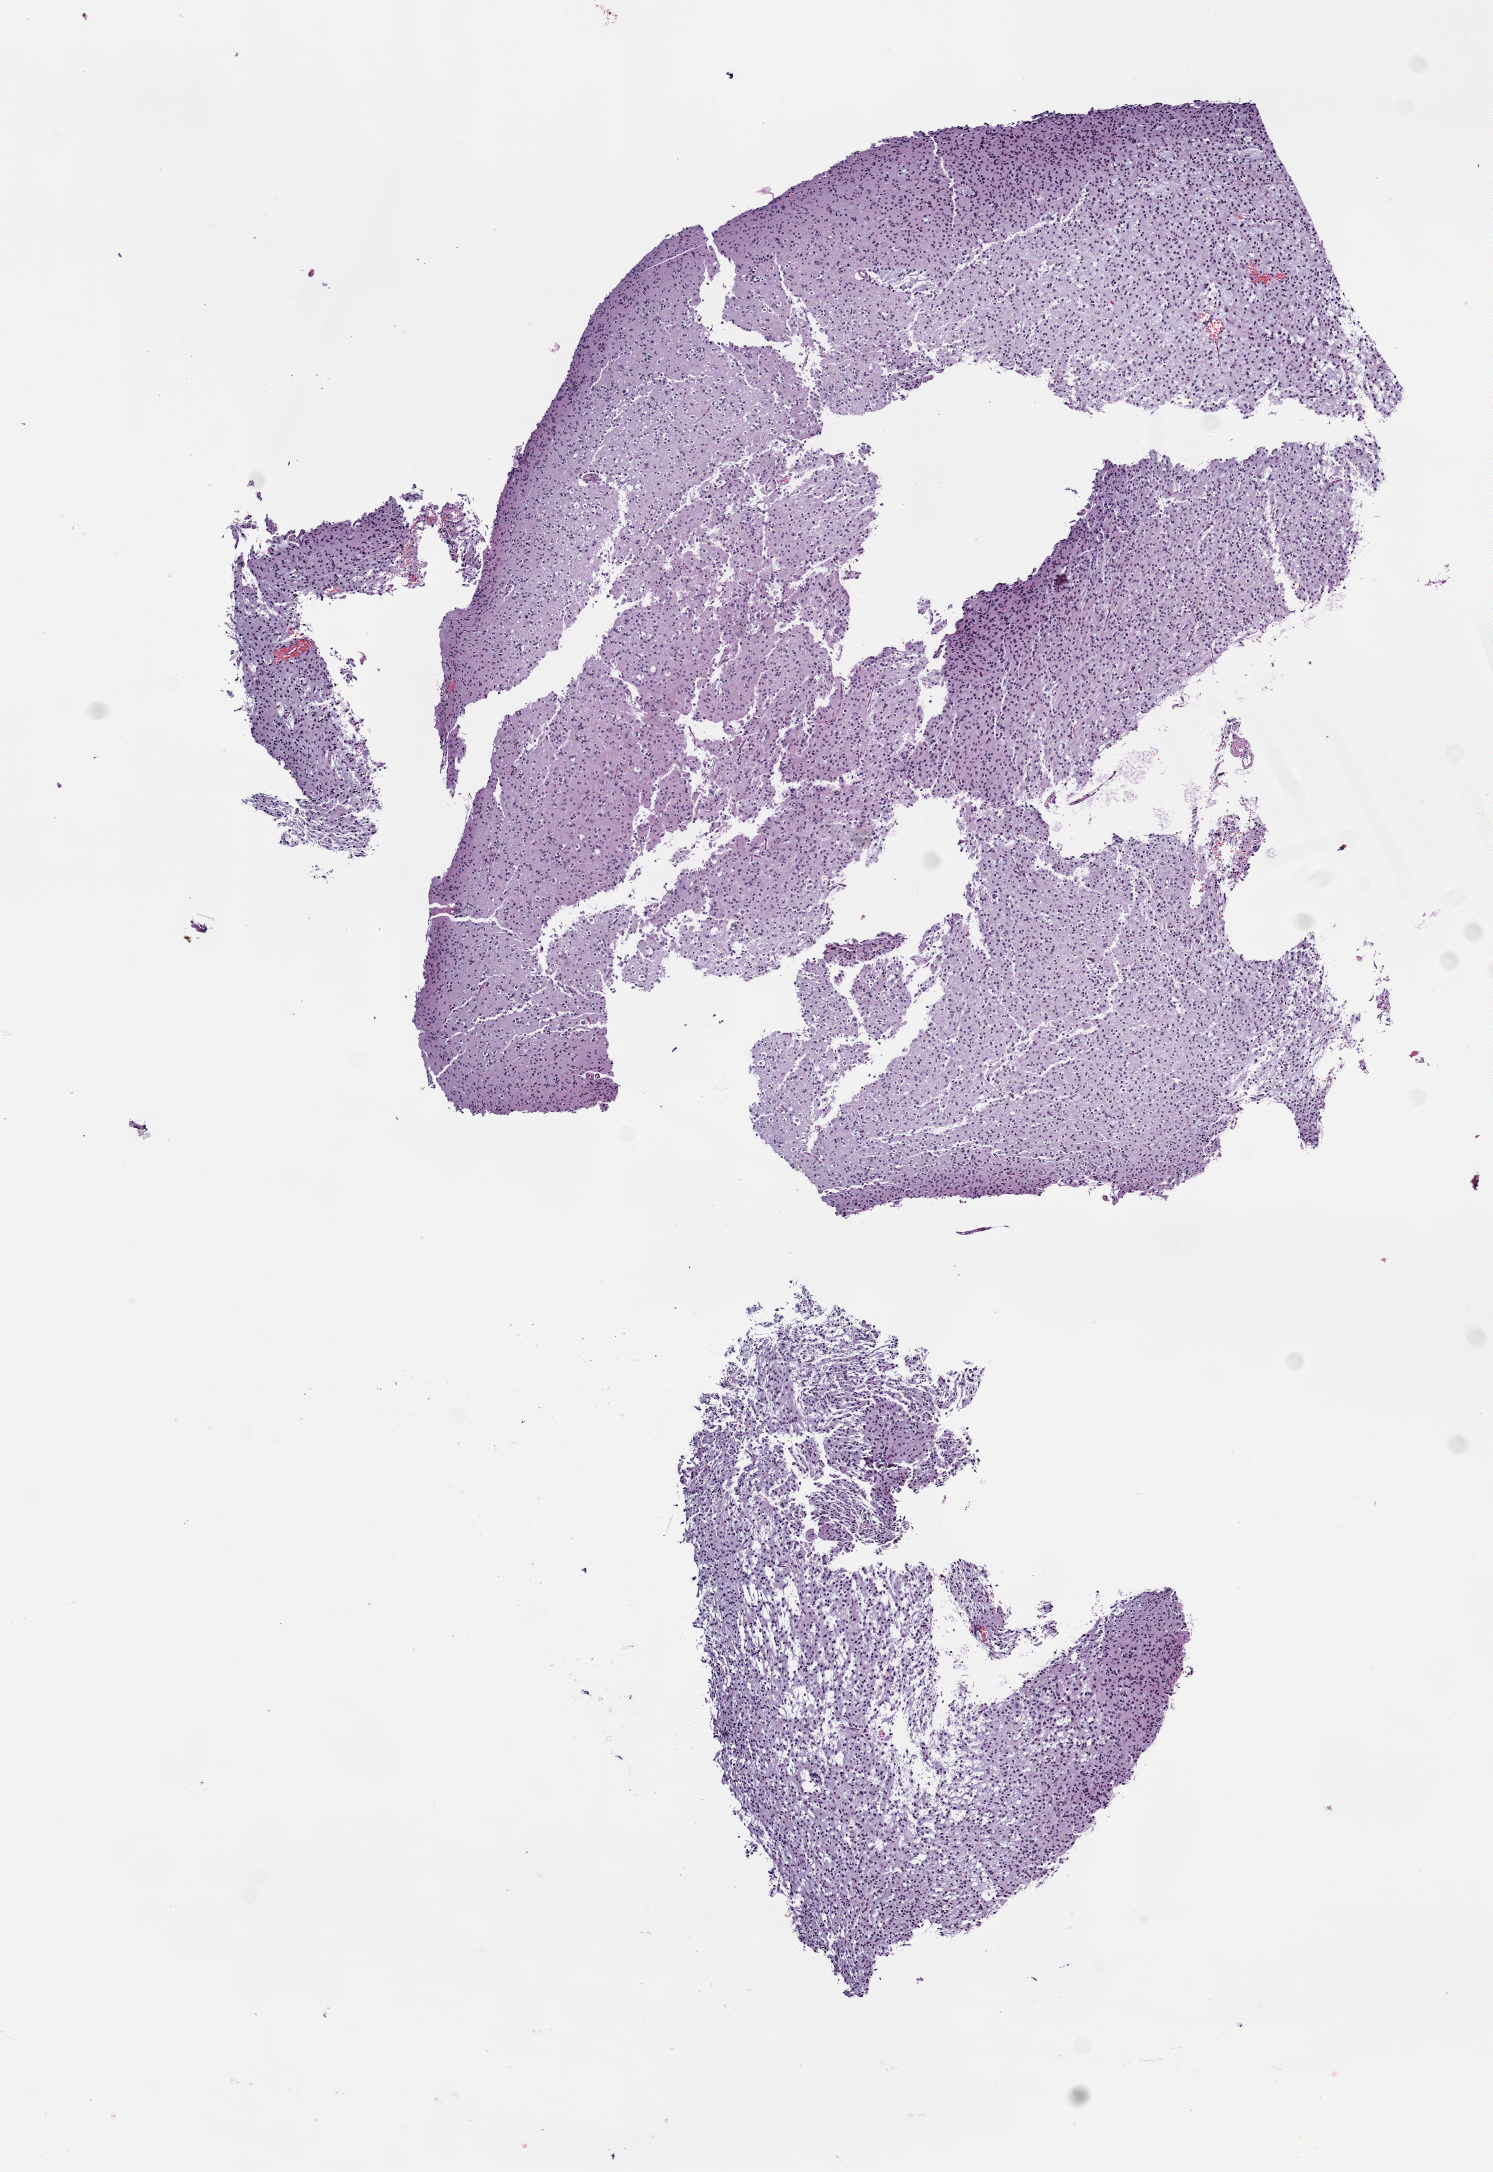
Digitized Hematoxylin and eosin (H&E) stained tissue section (whole slide), whole scanned area (about 6.0 x 8.8 mm, acquisition: 40x scan) shown as a low-resolution overview. Formalin-fixed paraffin-embedded (FFPE) diagnostic section. Brain, primary tumour sample. Female patient; age at initial diagnosis 50 years. Histologic grade: G2 (moderately differentiated).
Diagnosis: Oligodendroglioma, NOS (cerebrum).